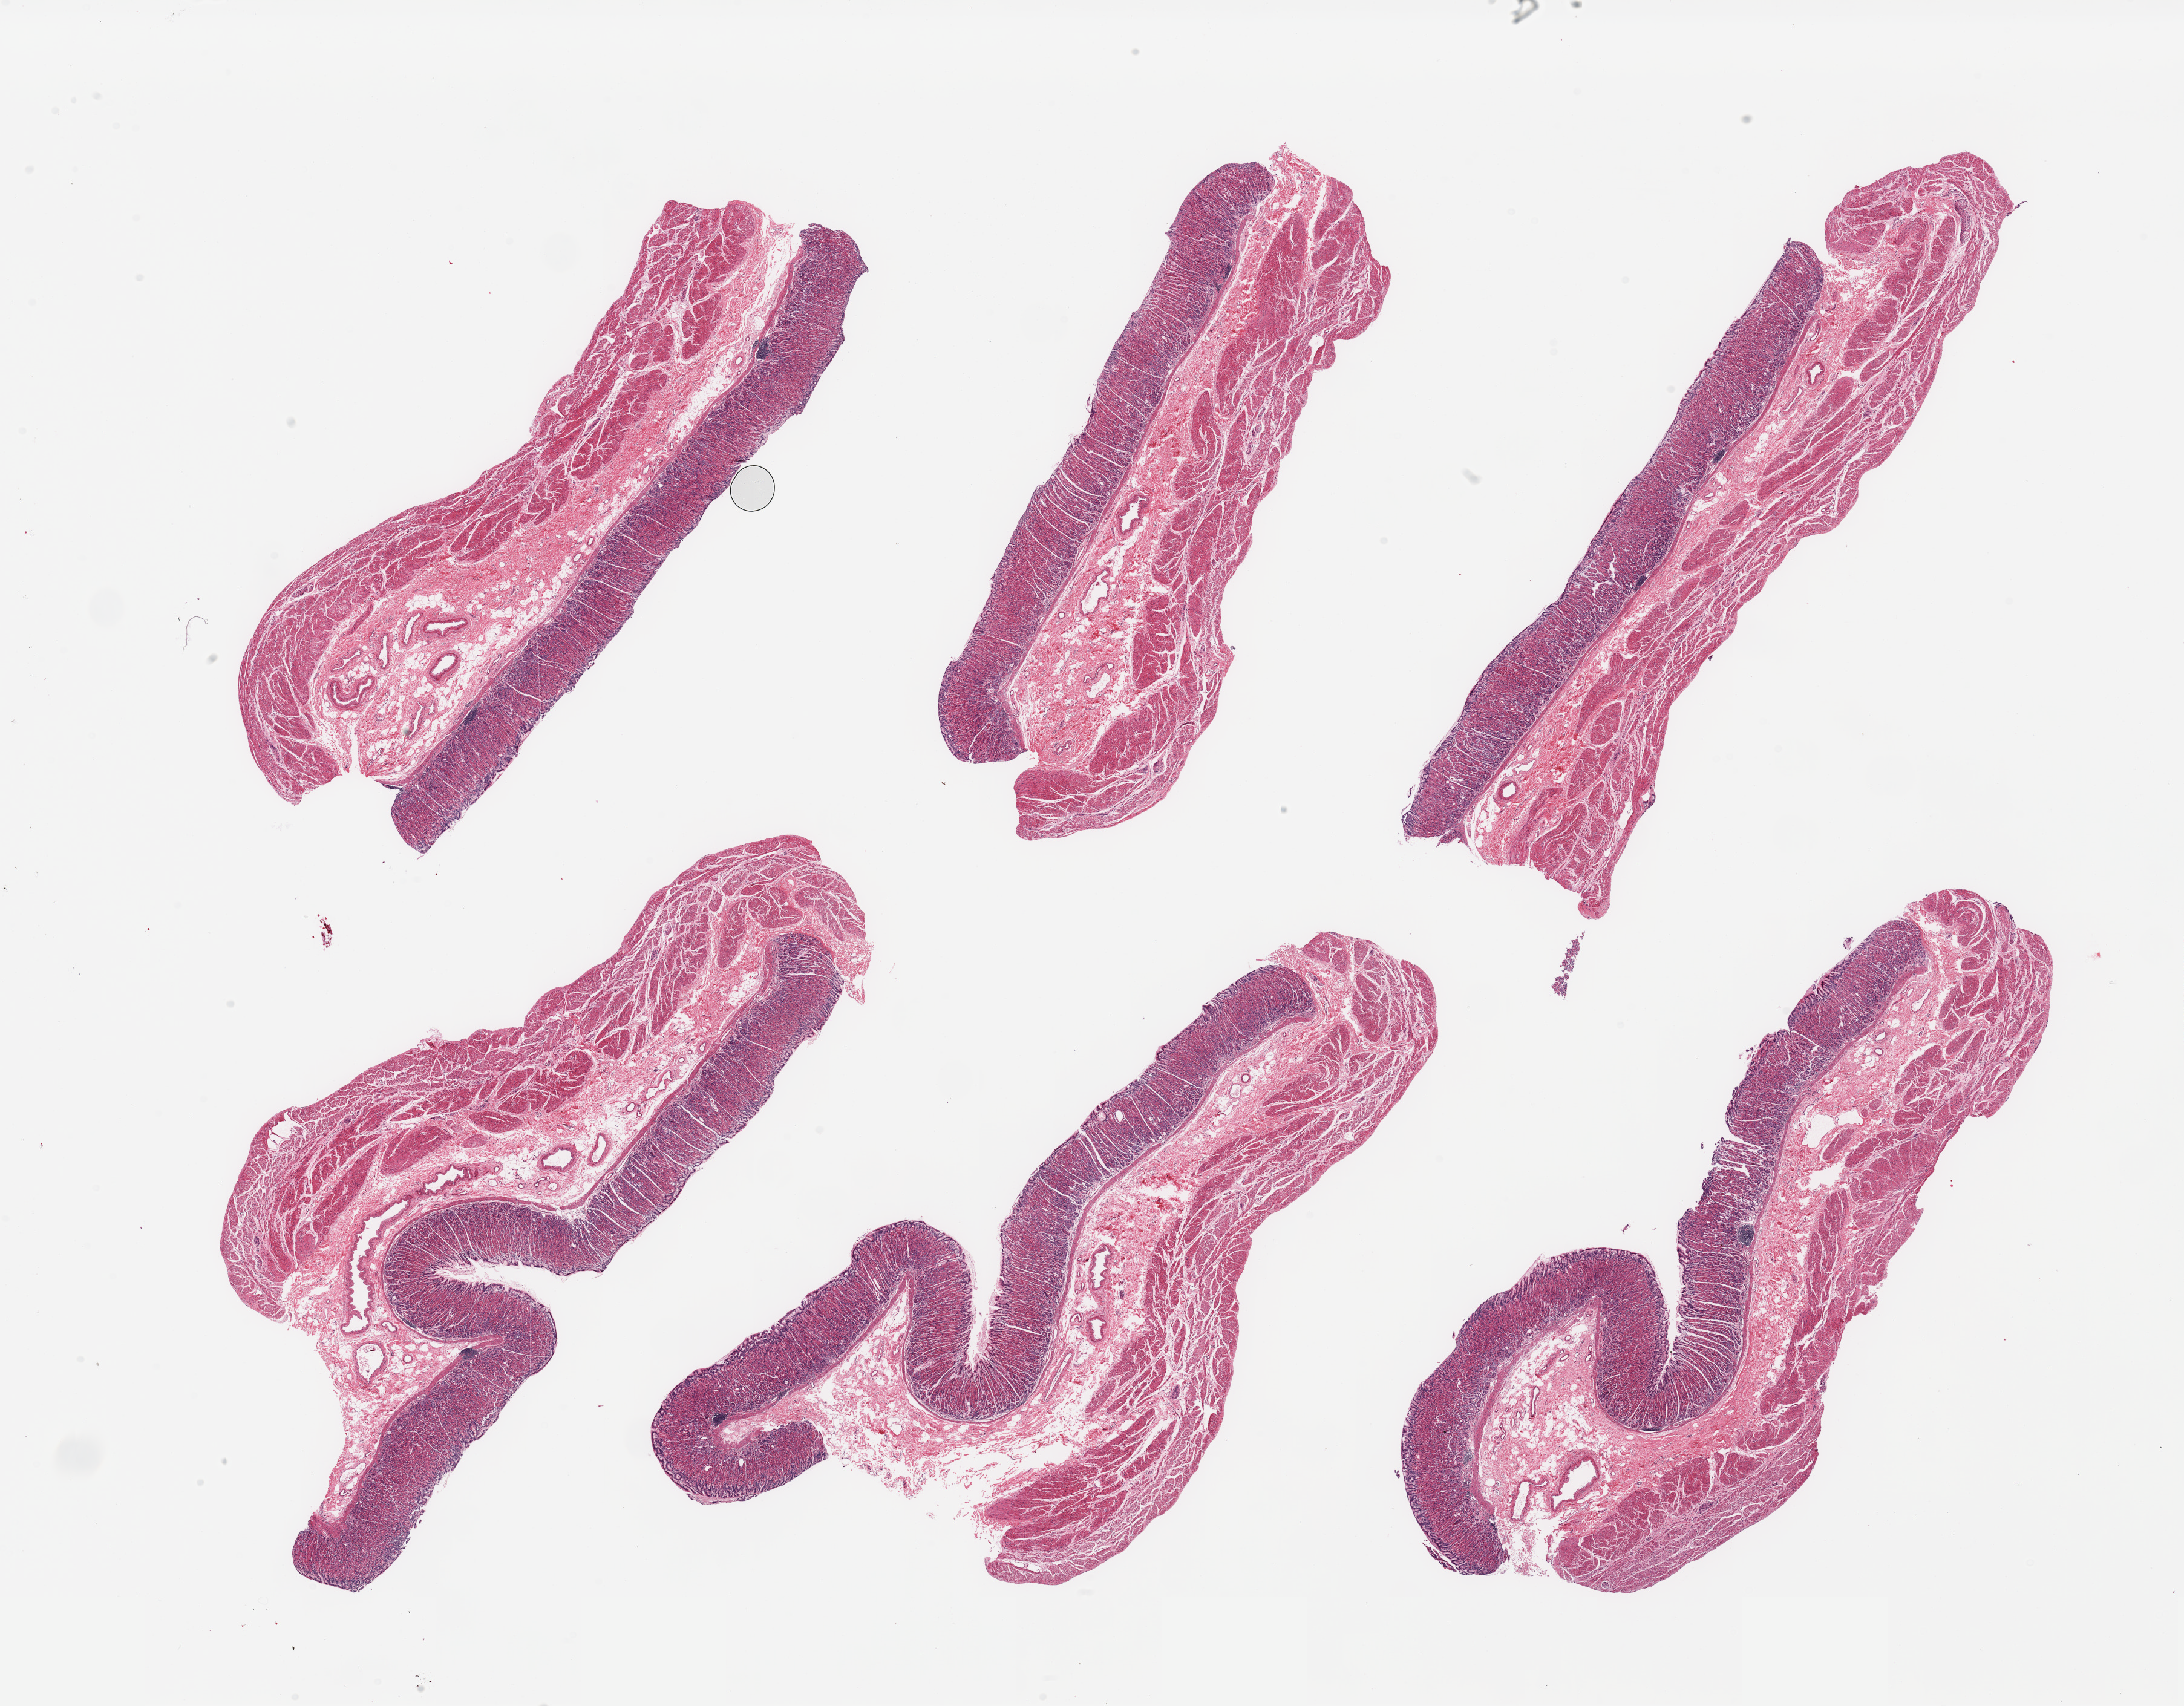
Hematoxylin and eosin (H&E) whole-slide image — low-resolution overview of the scanned area, about 28.5 x 22.3 mm. PAXgene-fixed paraffin-embedded (PFPE) section. Sampled site (target tissue): stomach. Donor tissue sample. Donor: female.
Review note (as recorded): 6 pieces; full thickness wall.